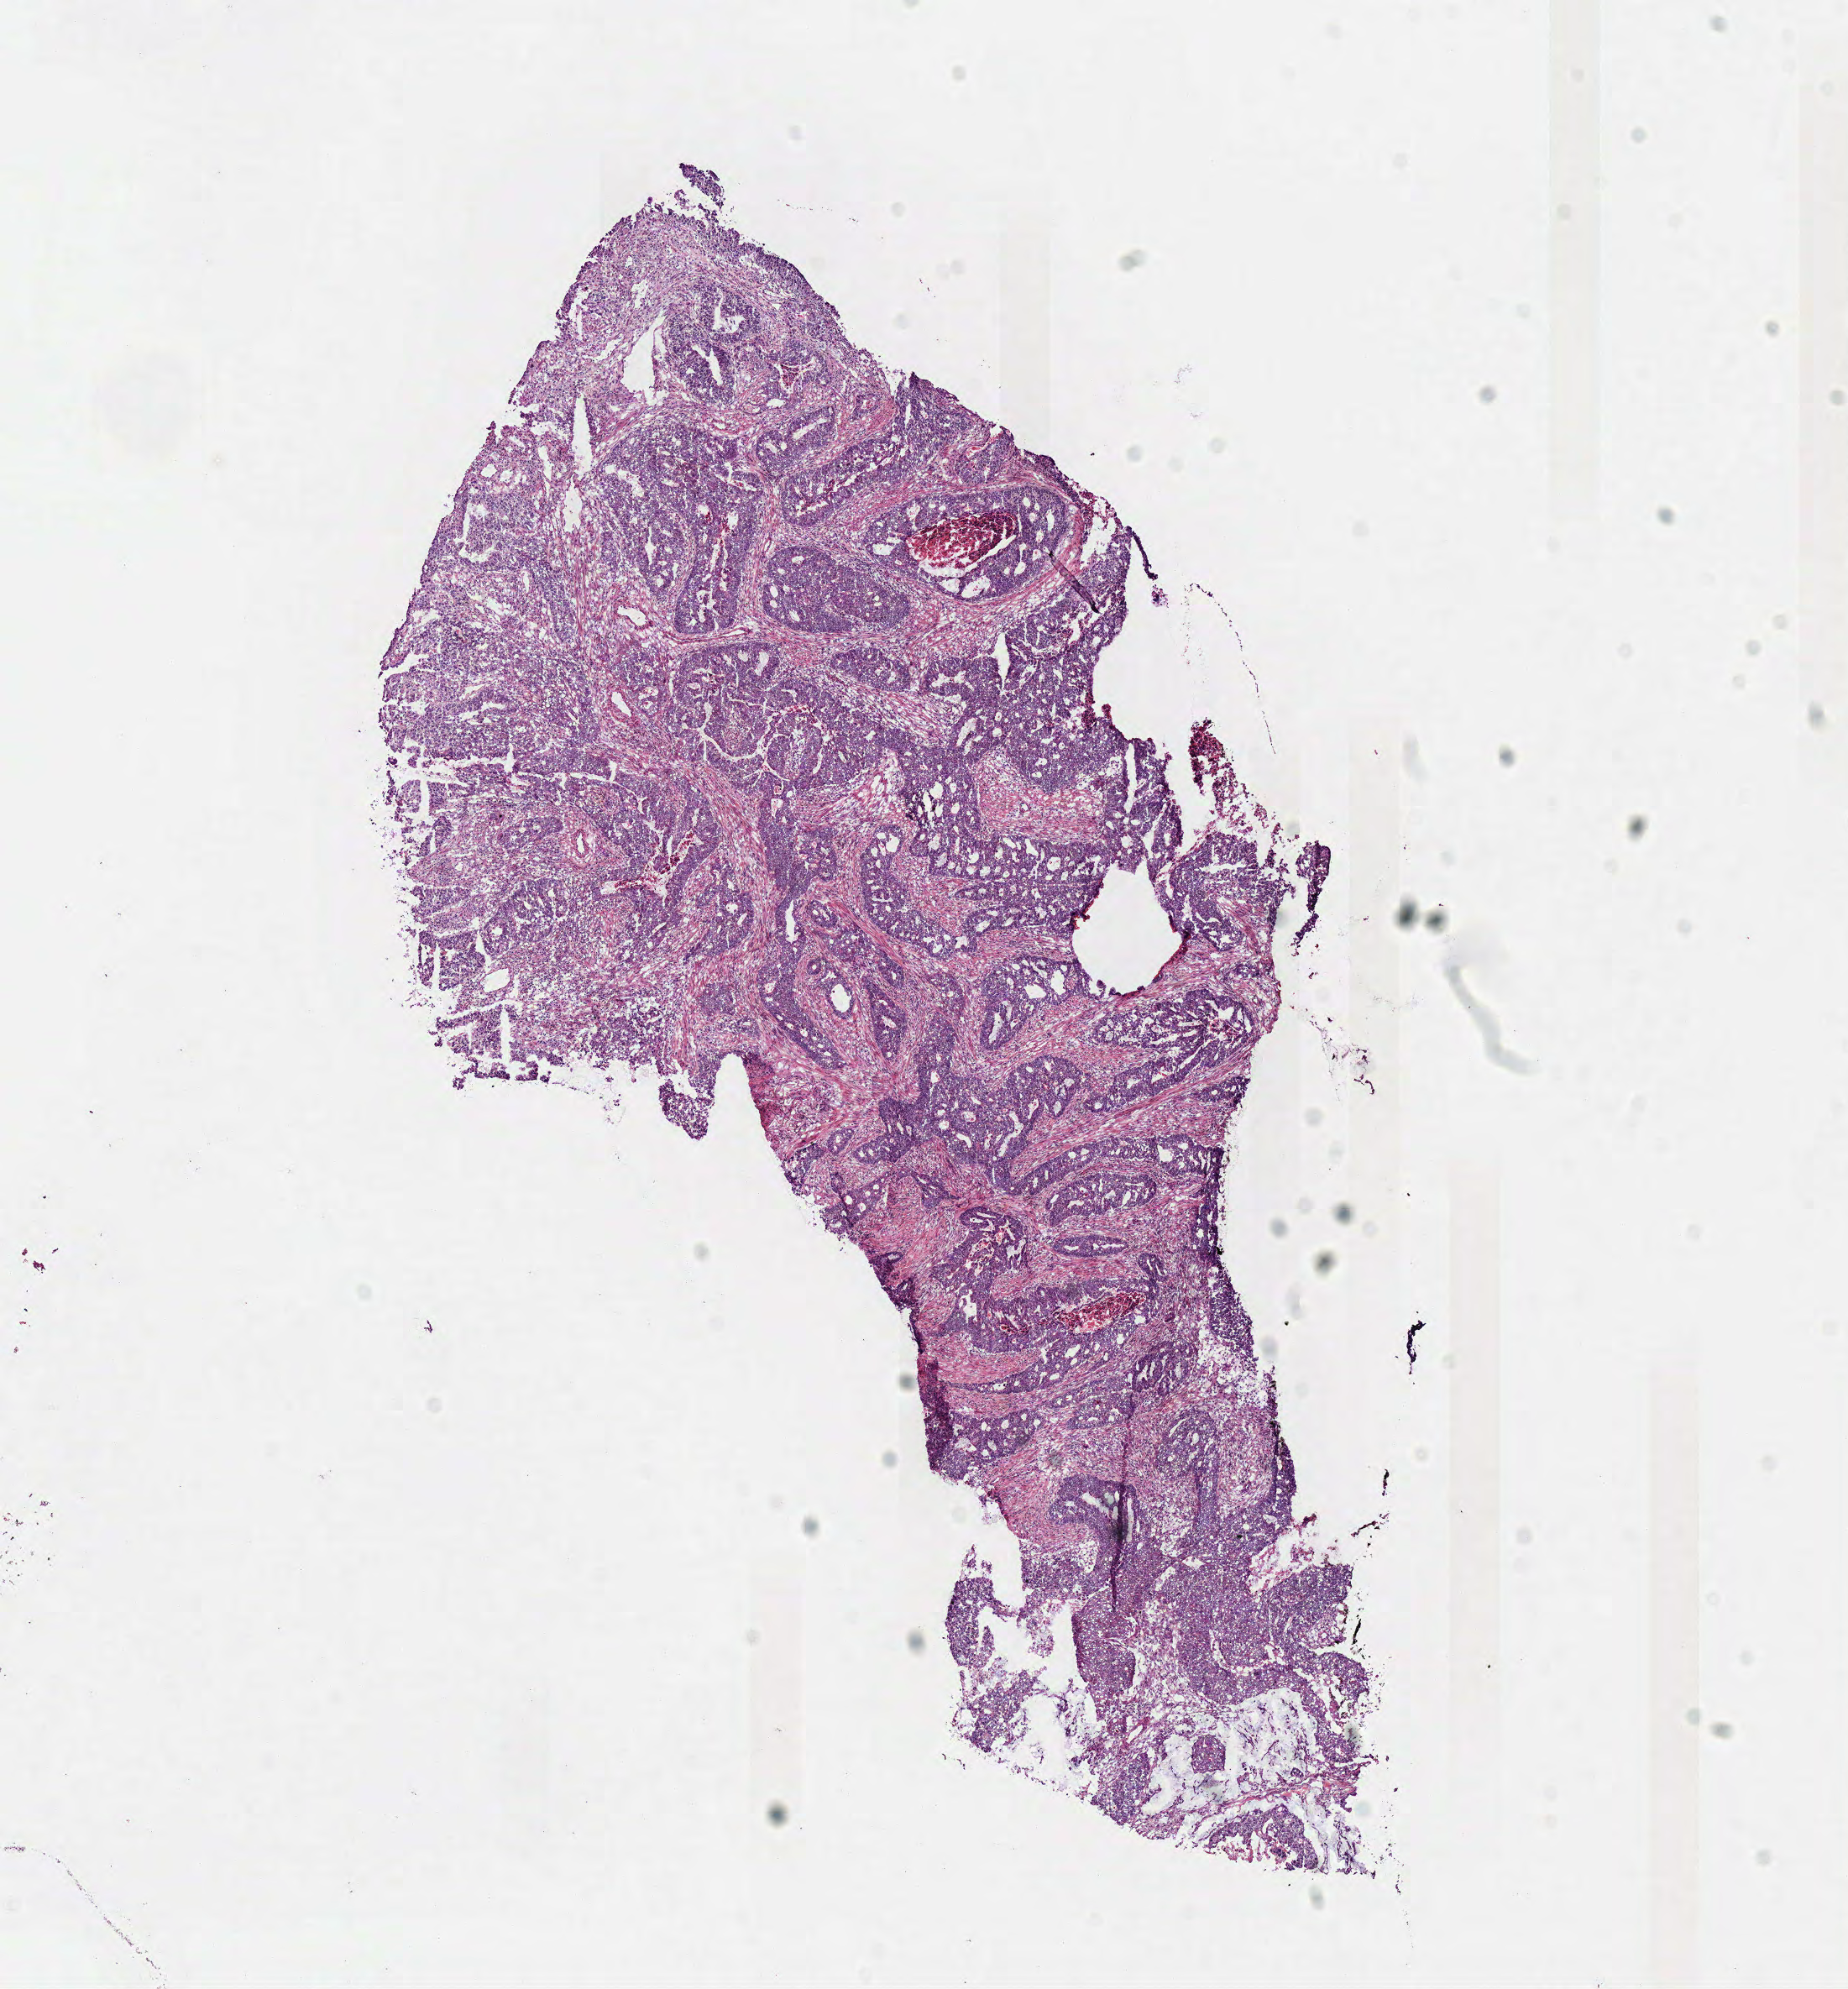
H&E-stained whole-slide image — whole scanned area (about 8.7 x 9.3 mm) shown as a low-resolution overview, frozen section from the top of the tissue portion, primary tumour sample from the colon. Male patient; age at initial diagnosis 62 years. Slide review estimates, as recorded: tumour cells 75%, tumour nuclei 80%, normal cells 0%, stromal cells 22%, necrosis 3%. Inflammatory infiltration, as recorded: lymphocyte infiltration 12%.
Histologic diagnosis: Adenocarcinoma, NOS. AJCC pathologic stage: IIIC.